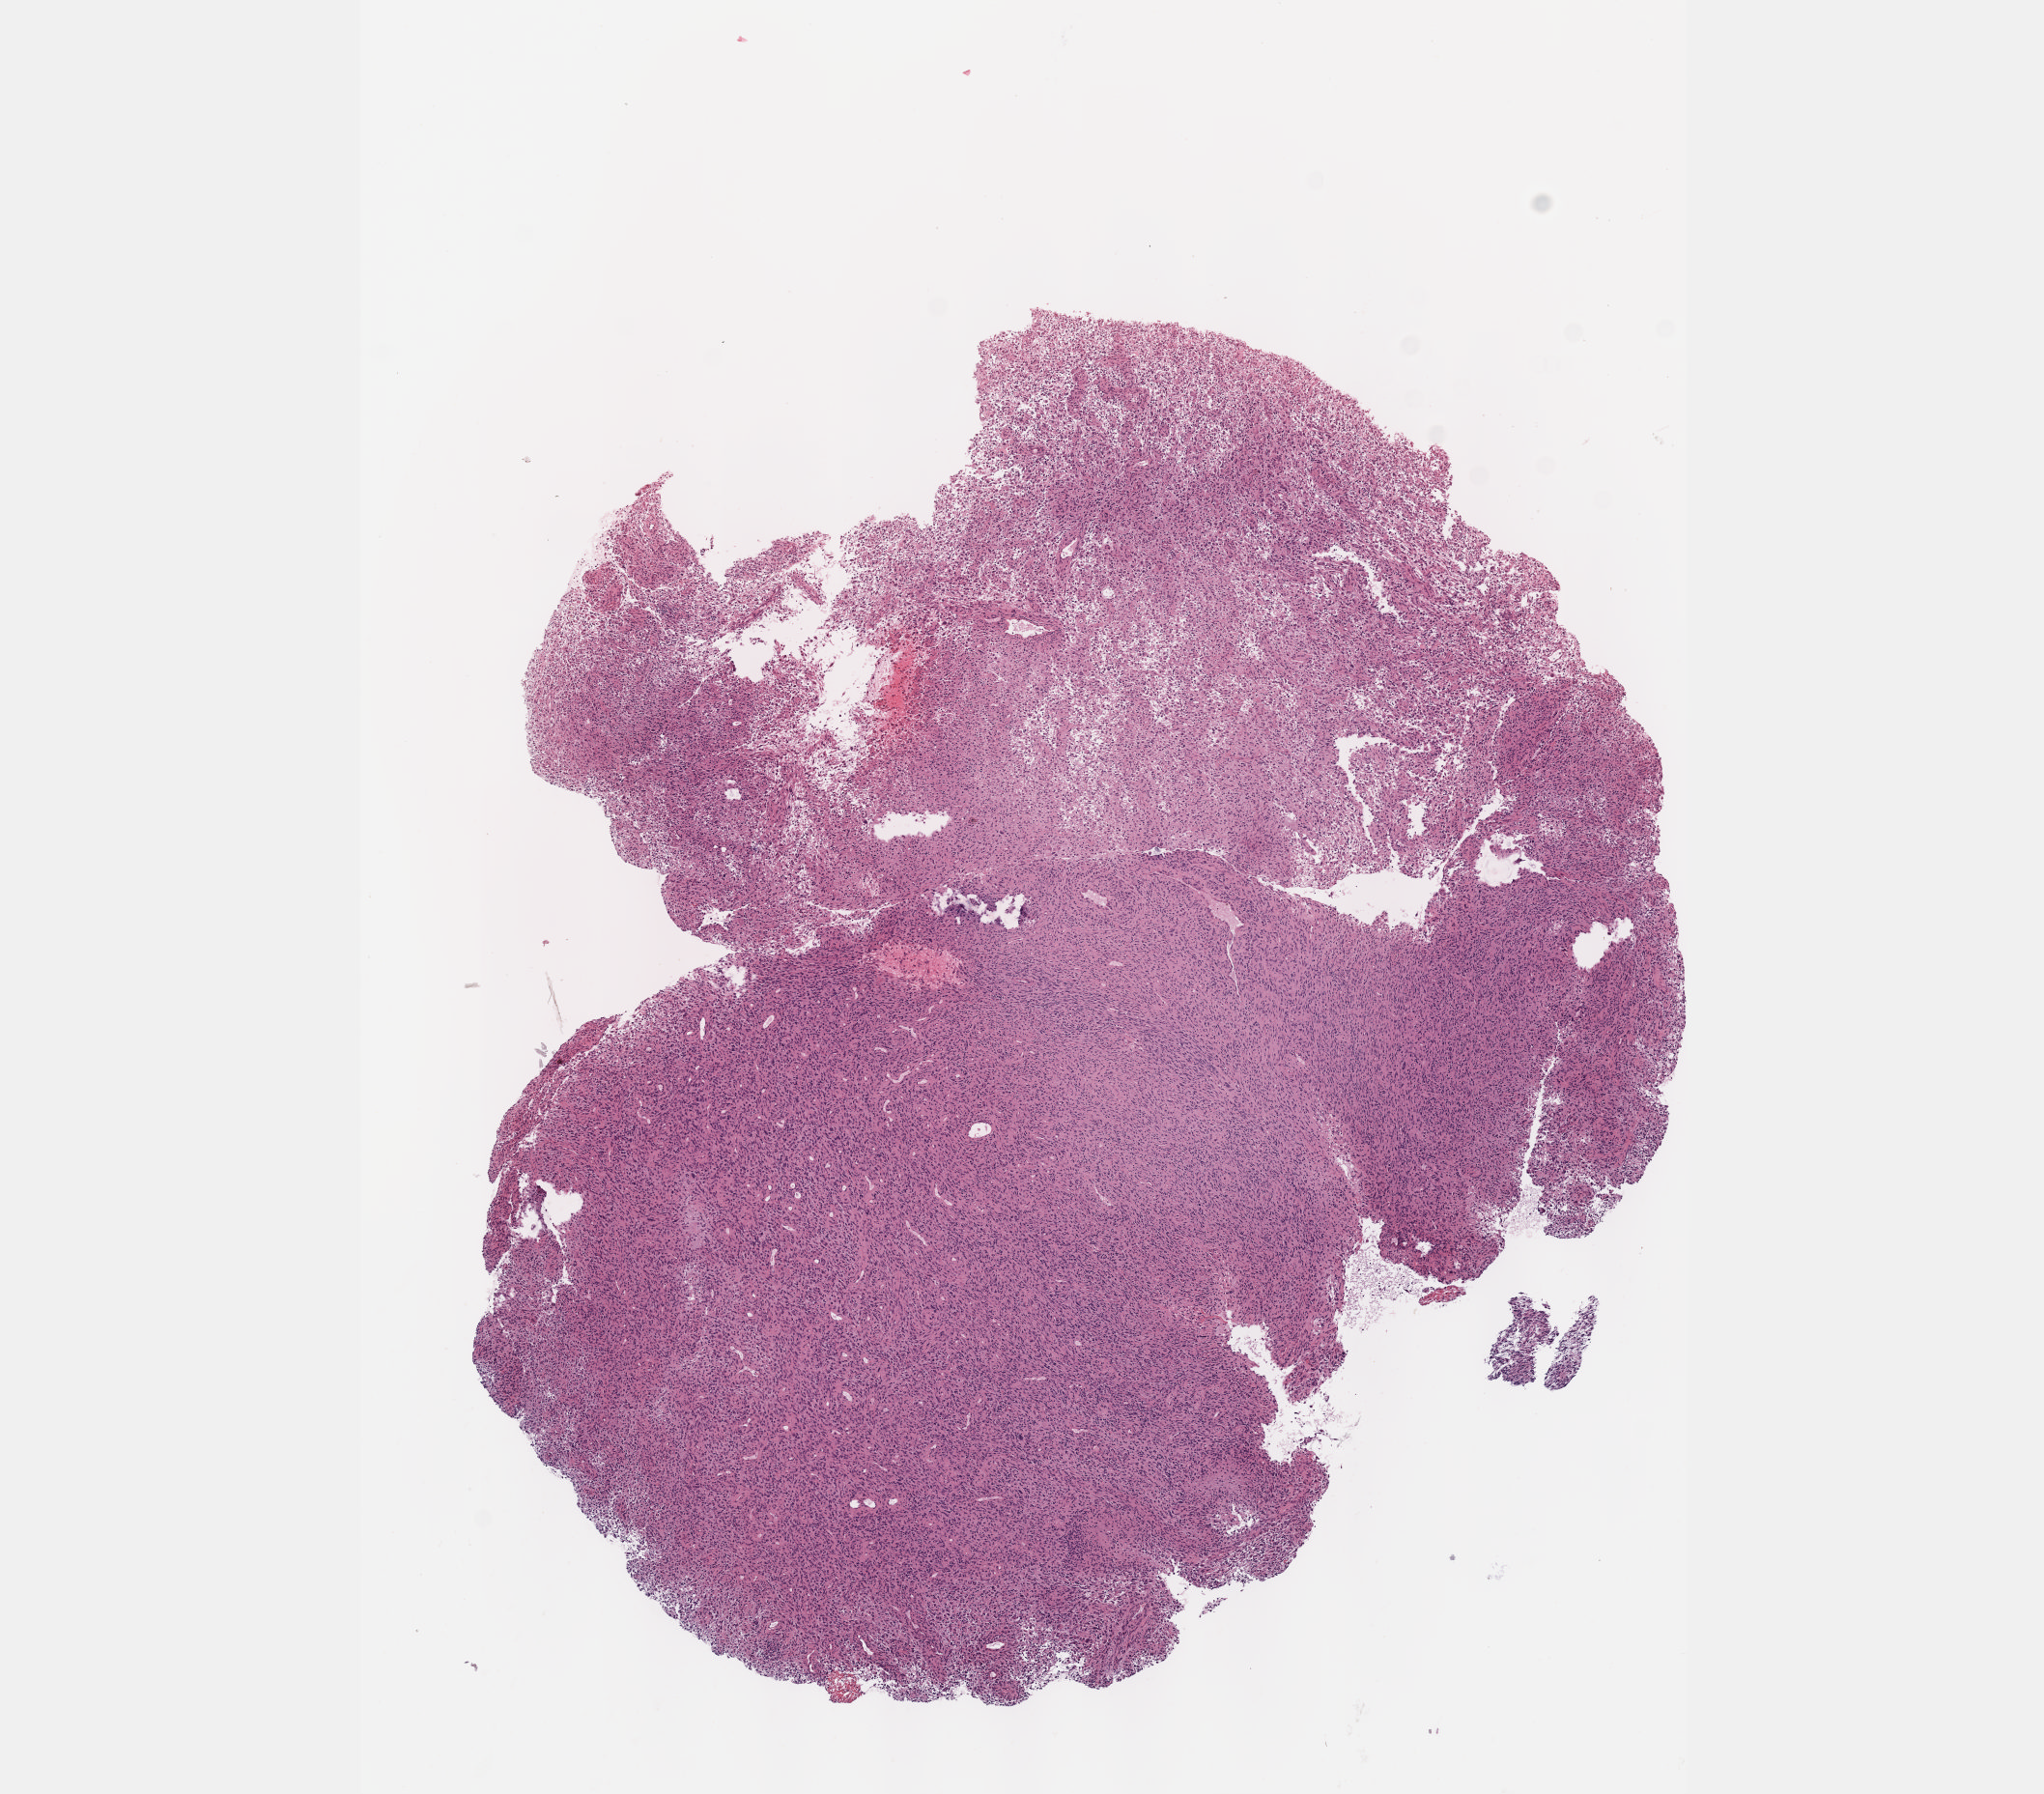
Whole-slide histology image, H&E-stained — whole scanned area (about 8.6 x 7.5 mm, slide scanned at 40x) shown as a low-resolution overview, formalin-fixed paraffin-embedded (FFPE) diagnostic section, sample: primary tumour, brain. Patient: female, age at initial diagnosis 60 years. Histologic grade: G3 (poorly differentiated).
Histologic diagnosis: Astrocytoma, anaplastic. Laterality: left.